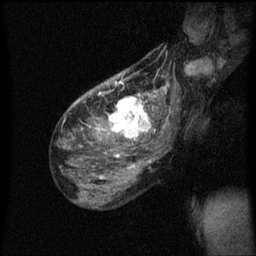
Breast MRI (dynamic contrast-enhanced), one sagittal slice. Position 36 of 60 along the scan axis. Dynamic contrast-enhanced series, image 2 of 3 at this slice position (ordered by acquisition). 1.5 T. TE 4.2 ms, TR 8.4 ms. 2 mm slice thickness. 256 × 256 image matrix, field of view 200 × 200 mm. Female patient, age 49 years.
Structures marked on this image (semi-automatically segmented with operator editing):
- analysis volume of interest (the breast-tissue region the enhancement analysis was run in; not a lesion): box from (x=103, y=90) to (x=157, y=151) px
- tumour enhancement mask (voxels above the 70 % enhancement threshold inside the analysis volume of interest): (x=109, y=94)–(x=156, y=141)